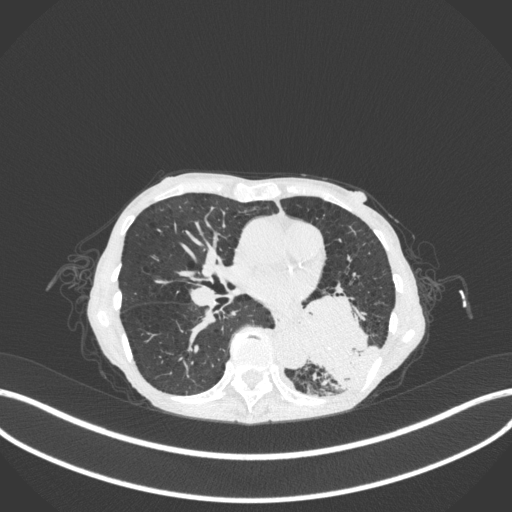
Chest CT, one axial slice; position 132 of 347 along the scan axis; reconstruction kernel B31f; lung window (W 1500 / L -600 HU); 512 × 512 image matrix, field of view 400 × 400 mm. Female patient, age 70 years. From the clinical record (not read from this slice): clinical TNM (as recorded): T3 N0 M0.
Structures marked on this image (rectangle marked by the reading radiologist):
- lung tumour (recorded histology: small cell carcinoma): bounding box <294,285,375,390> (left, top, right, bottom; pixels)